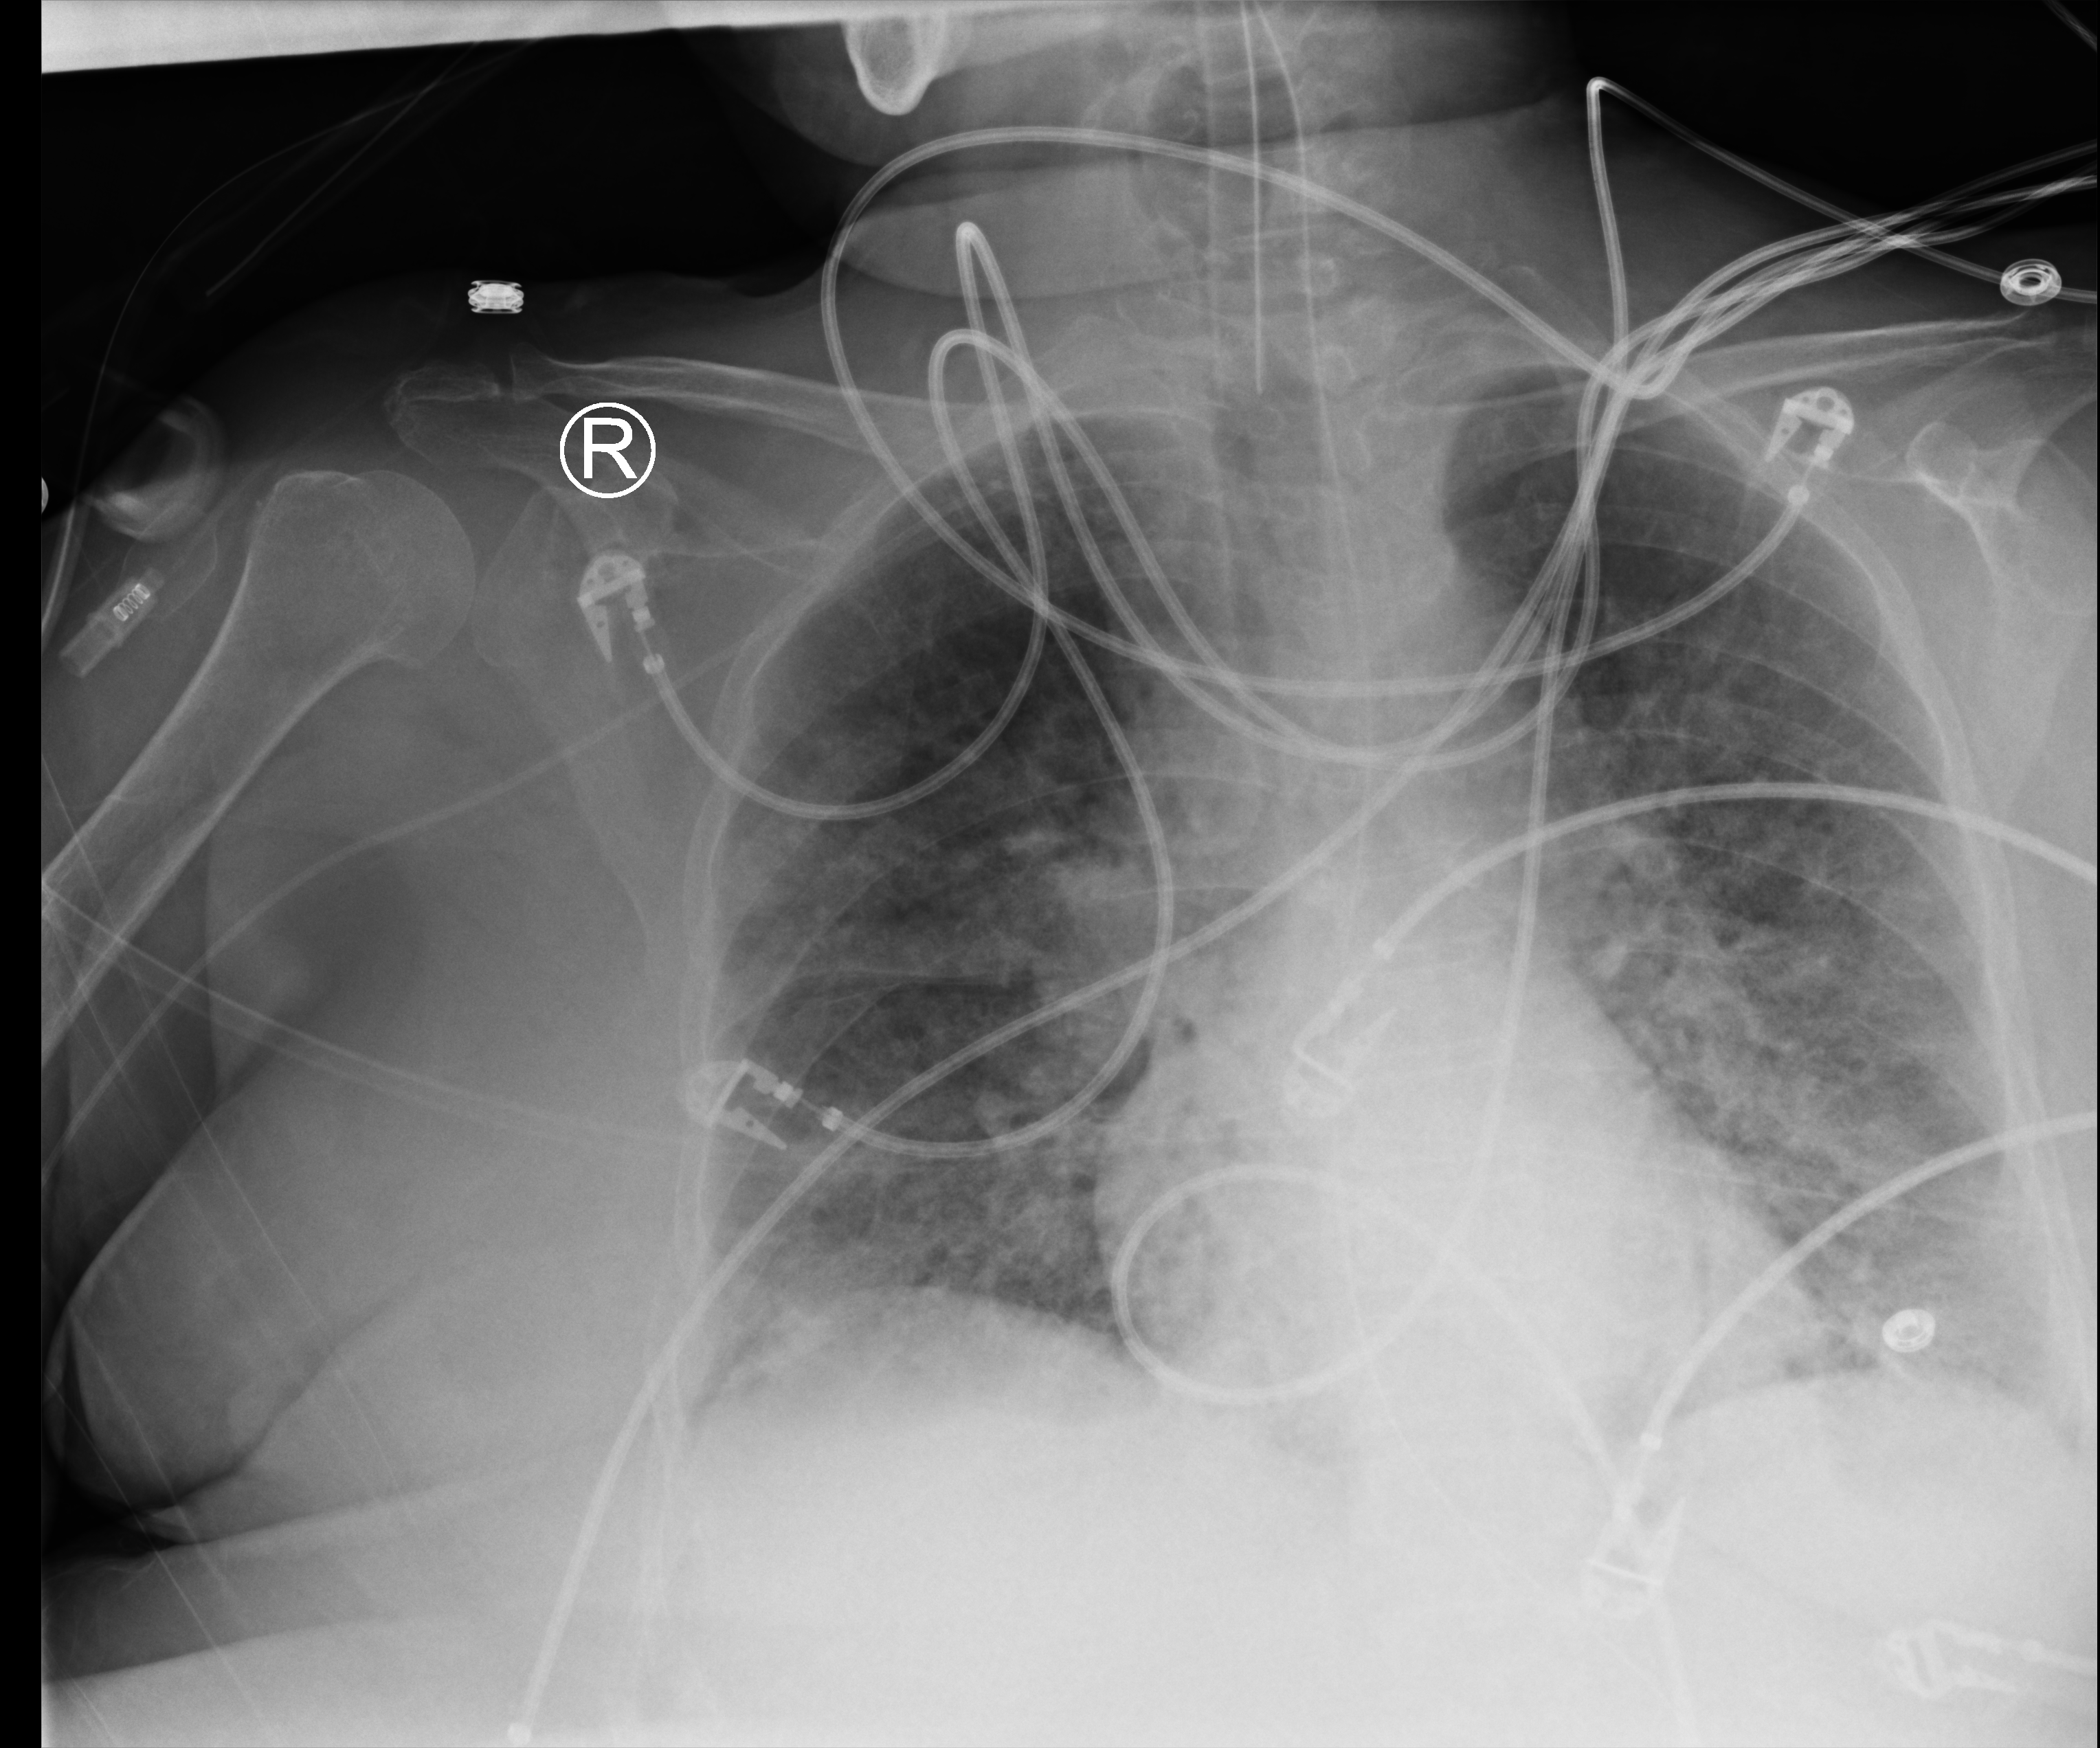
Bedside chest radiograph (computed radiography), anteroposterior (AP) projection. Patient hospitalised with COVID-19; female, aged 60–74 years.
From the hospital-stay record, not from the radiograph (when in the stay this image was taken is not recorded): hypertension (admission record): yes; admitted to intensive care during this hospital stay: yes.